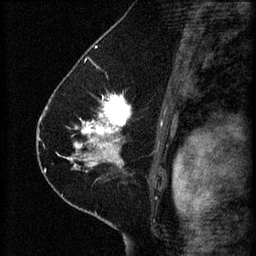
Breast MRI (dynamic contrast-enhanced), one sagittal slice. Position 39 of 60 along the scan axis. 3 images stored at this slice position (order not interpretable as contrast timing). 1.5 T. TE 4.2 ms, TR 8.2 ms. 256 × 256 image matrix, field of view 180 × 180 mm. Patient: female, 41 years.
Outlined on this slice (semi-automatic segmentation, software-assisted and operator-edited):
- analysis volume of interest (the breast-tissue region the enhancement analysis was run in; not a lesion): bounding box [x1, y1, x2, y2] px = [67, 94, 165, 173]
- tumour enhancement mask (voxels above the 70 % enhancement threshold inside the analysis volume of interest): [71, 94, 163, 167]